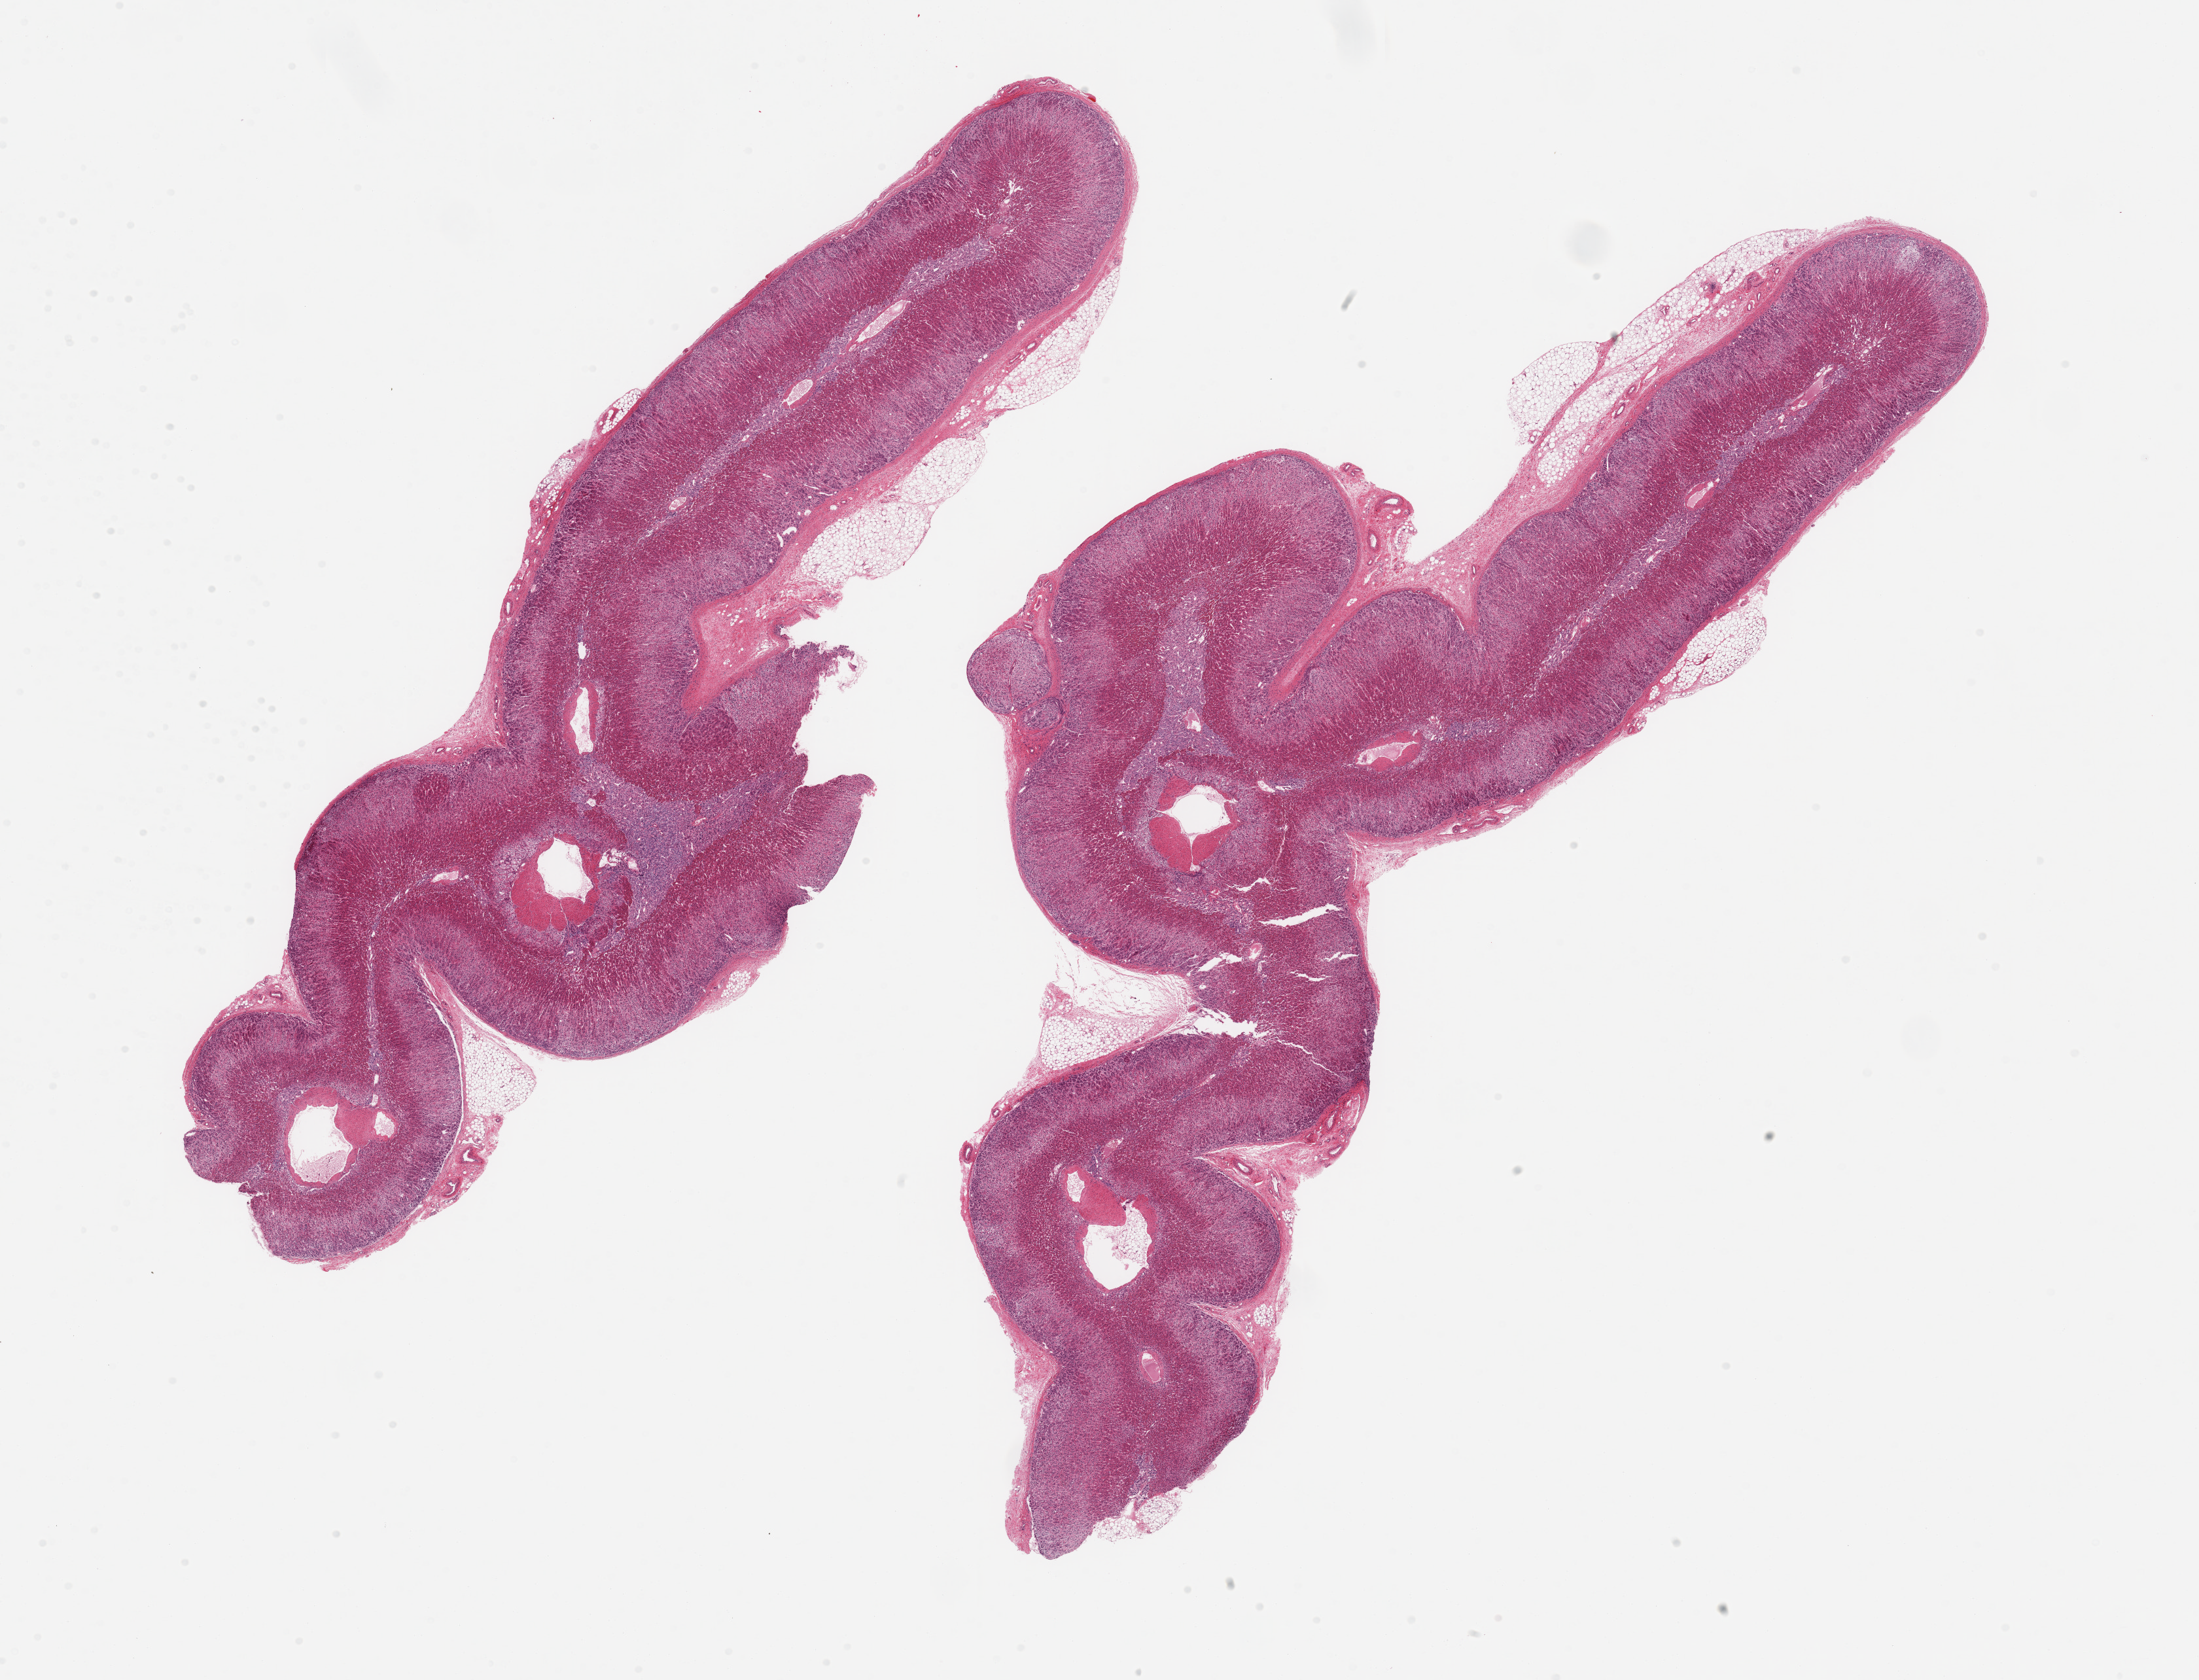
Haematoxylin and eosin whole-slide image, a low-resolution overview of the entire scanned area, about 26.6 x 20.3 mm, PAXgene-fixed, paraffin-embedded tissue, target tissue: adrenal gland, tissue donor sample. Male donor.
Pathologist's review note for this sample: 2 pieces; cortex and medulla with 5-10% attached fat.